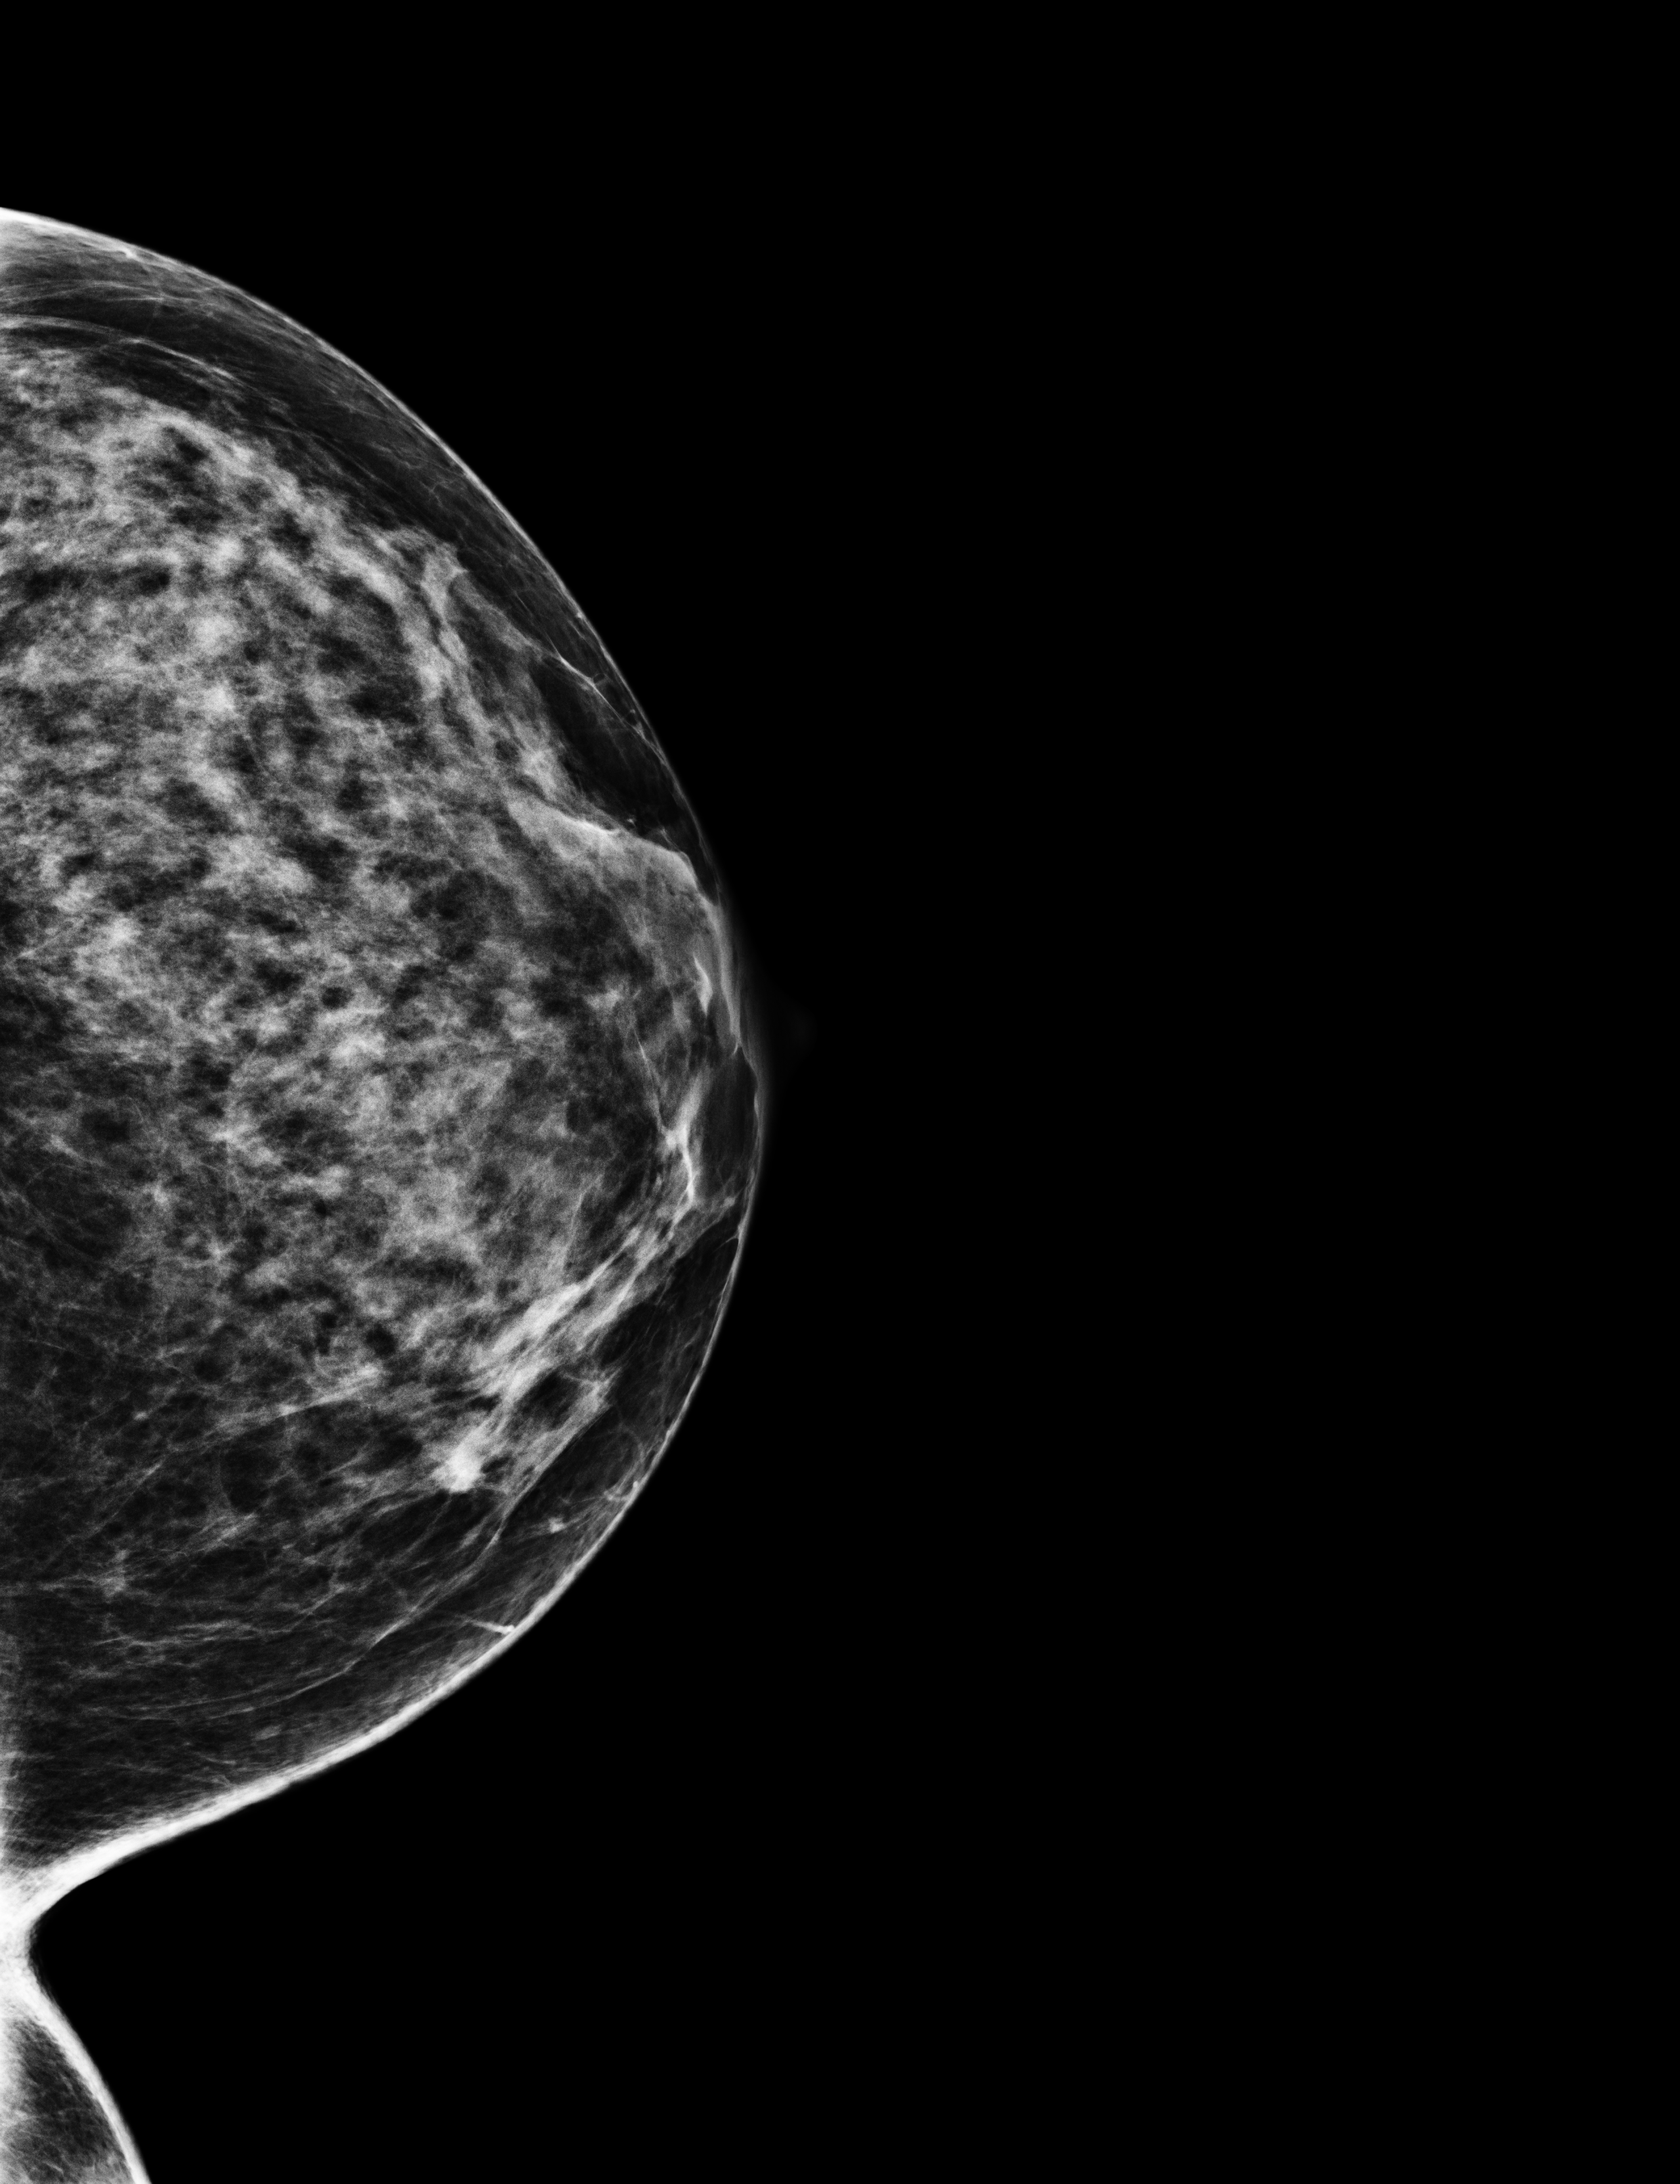
Digital mammogram (FFDM); left breast; craniocaudal (CC) view; screening examination; compressed breast thickness 54 mm; system: Selenia Dimensions. Female patient, age 59 years.
BI-RADS breast density category at the screening exam (both breasts, scale 1–4): 3. Final BI-RADS category for the screening round (tomosynthesis exam, both breasts): category 1. Recall: no recall after this screen.